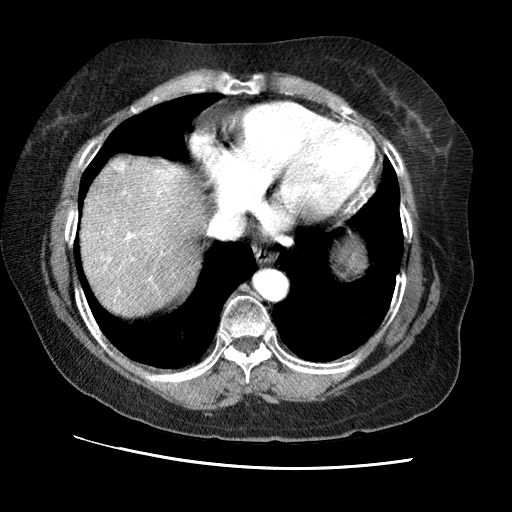
Contrast-enhanced abdominal CT (liver protocol), one axial slice. Slice 65 of 65 in the series (ordered by position). Reconstruction kernel STANDARD. Soft-tissue window (W 400 / L 40 HU). 2.5 mm slice thickness. 512 × 512 image matrix. From the clinical record (not read from this slice): diagnosis: hepatocellular carcinoma (patient treated with transarterial chemoembolisation; whether this scan precedes or follows treatment is not stated here); TNM stage (as recorded): Stage-II; Child-Pugh class: A; tumour differentiation: no biopsy; tumour nodularity: multinodular.
Structures marked on this image (semi-automatically segmented with operator editing):
- liver parenchyma outside the tumour (the mass and vessels are separate outlines, so this box may not span the whole liver): bounding box (x1, y1, x2, y2) in pixels: (80, 156, 204, 316)
- mass: (111, 158, 125, 172)
- liver vessels: (101, 167, 177, 293)